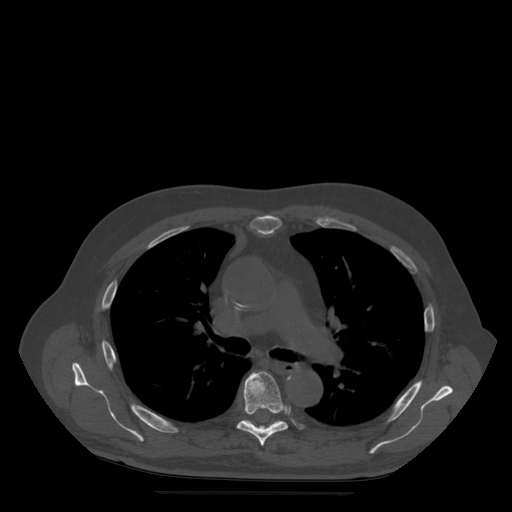
CT including the spine, one axial slice; slice 352 of 522 in the series (ordered by position); bone window (W 1800 / L 400 HU); 512 × 512 image matrix, field of view 420 × 420 mm. Patient age 72 years. Case-level facts recorded for this patient, not image findings: primary cancer: prostate.
Outlined on this slice (semi-automatically segmented with operator editing):
- T6 vertebra: box from (x=237, y=372) to (x=291, y=446) px
- T7 vertebra: (x=244, y=420)–(x=283, y=428)